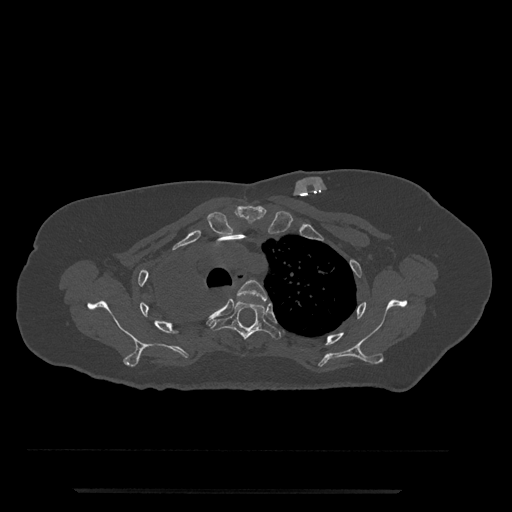
CT including the spine, one axial slice. Reconstruction kernel Br40s/3. Bone window (W 1800 / L 400 HU). 0.5 mm slice thickness. 512 × 512 image matrix. Patient: female, 51 years. Case-level facts recorded for this patient, not image findings: primary cancer: neuro; vertebrae with lytic lesions (as recorded): T8.
Structures marked on this image (semi-automatically segmented with operator editing):
- T3 vertebra: bounding box <237,279,267,302> (left, top, right, bottom; pixels)
- T4 vertebra: <210,300,281,340>